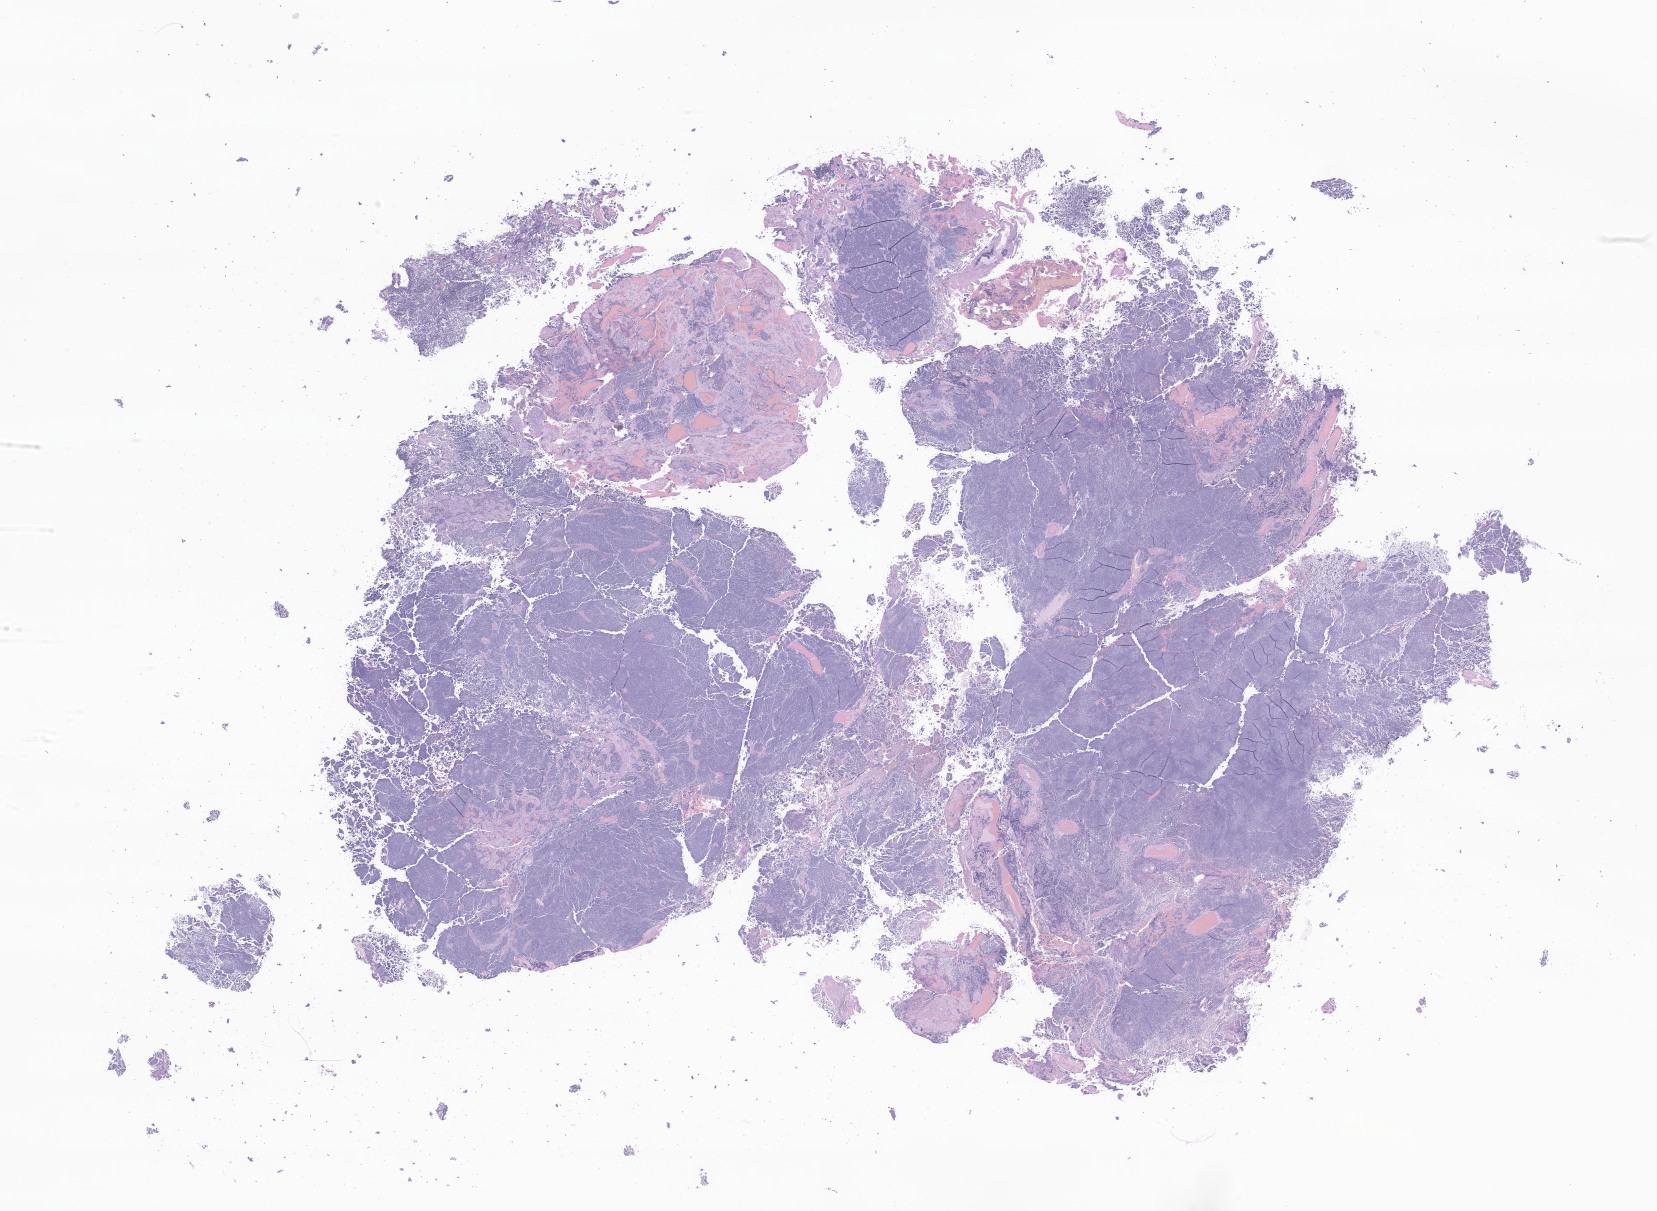
Whole-slide image, H&E stain of tumor tissue from the brain — a low-resolution overview of the entire scanned area, about 27.9 x 20.4 mm; formalin-fixed paraffin-embedded section. Patient male; age 38 months (3 years 2 months).
• diagnosis (ICD-O-3 morphology term): Medulloblastoma, NOS